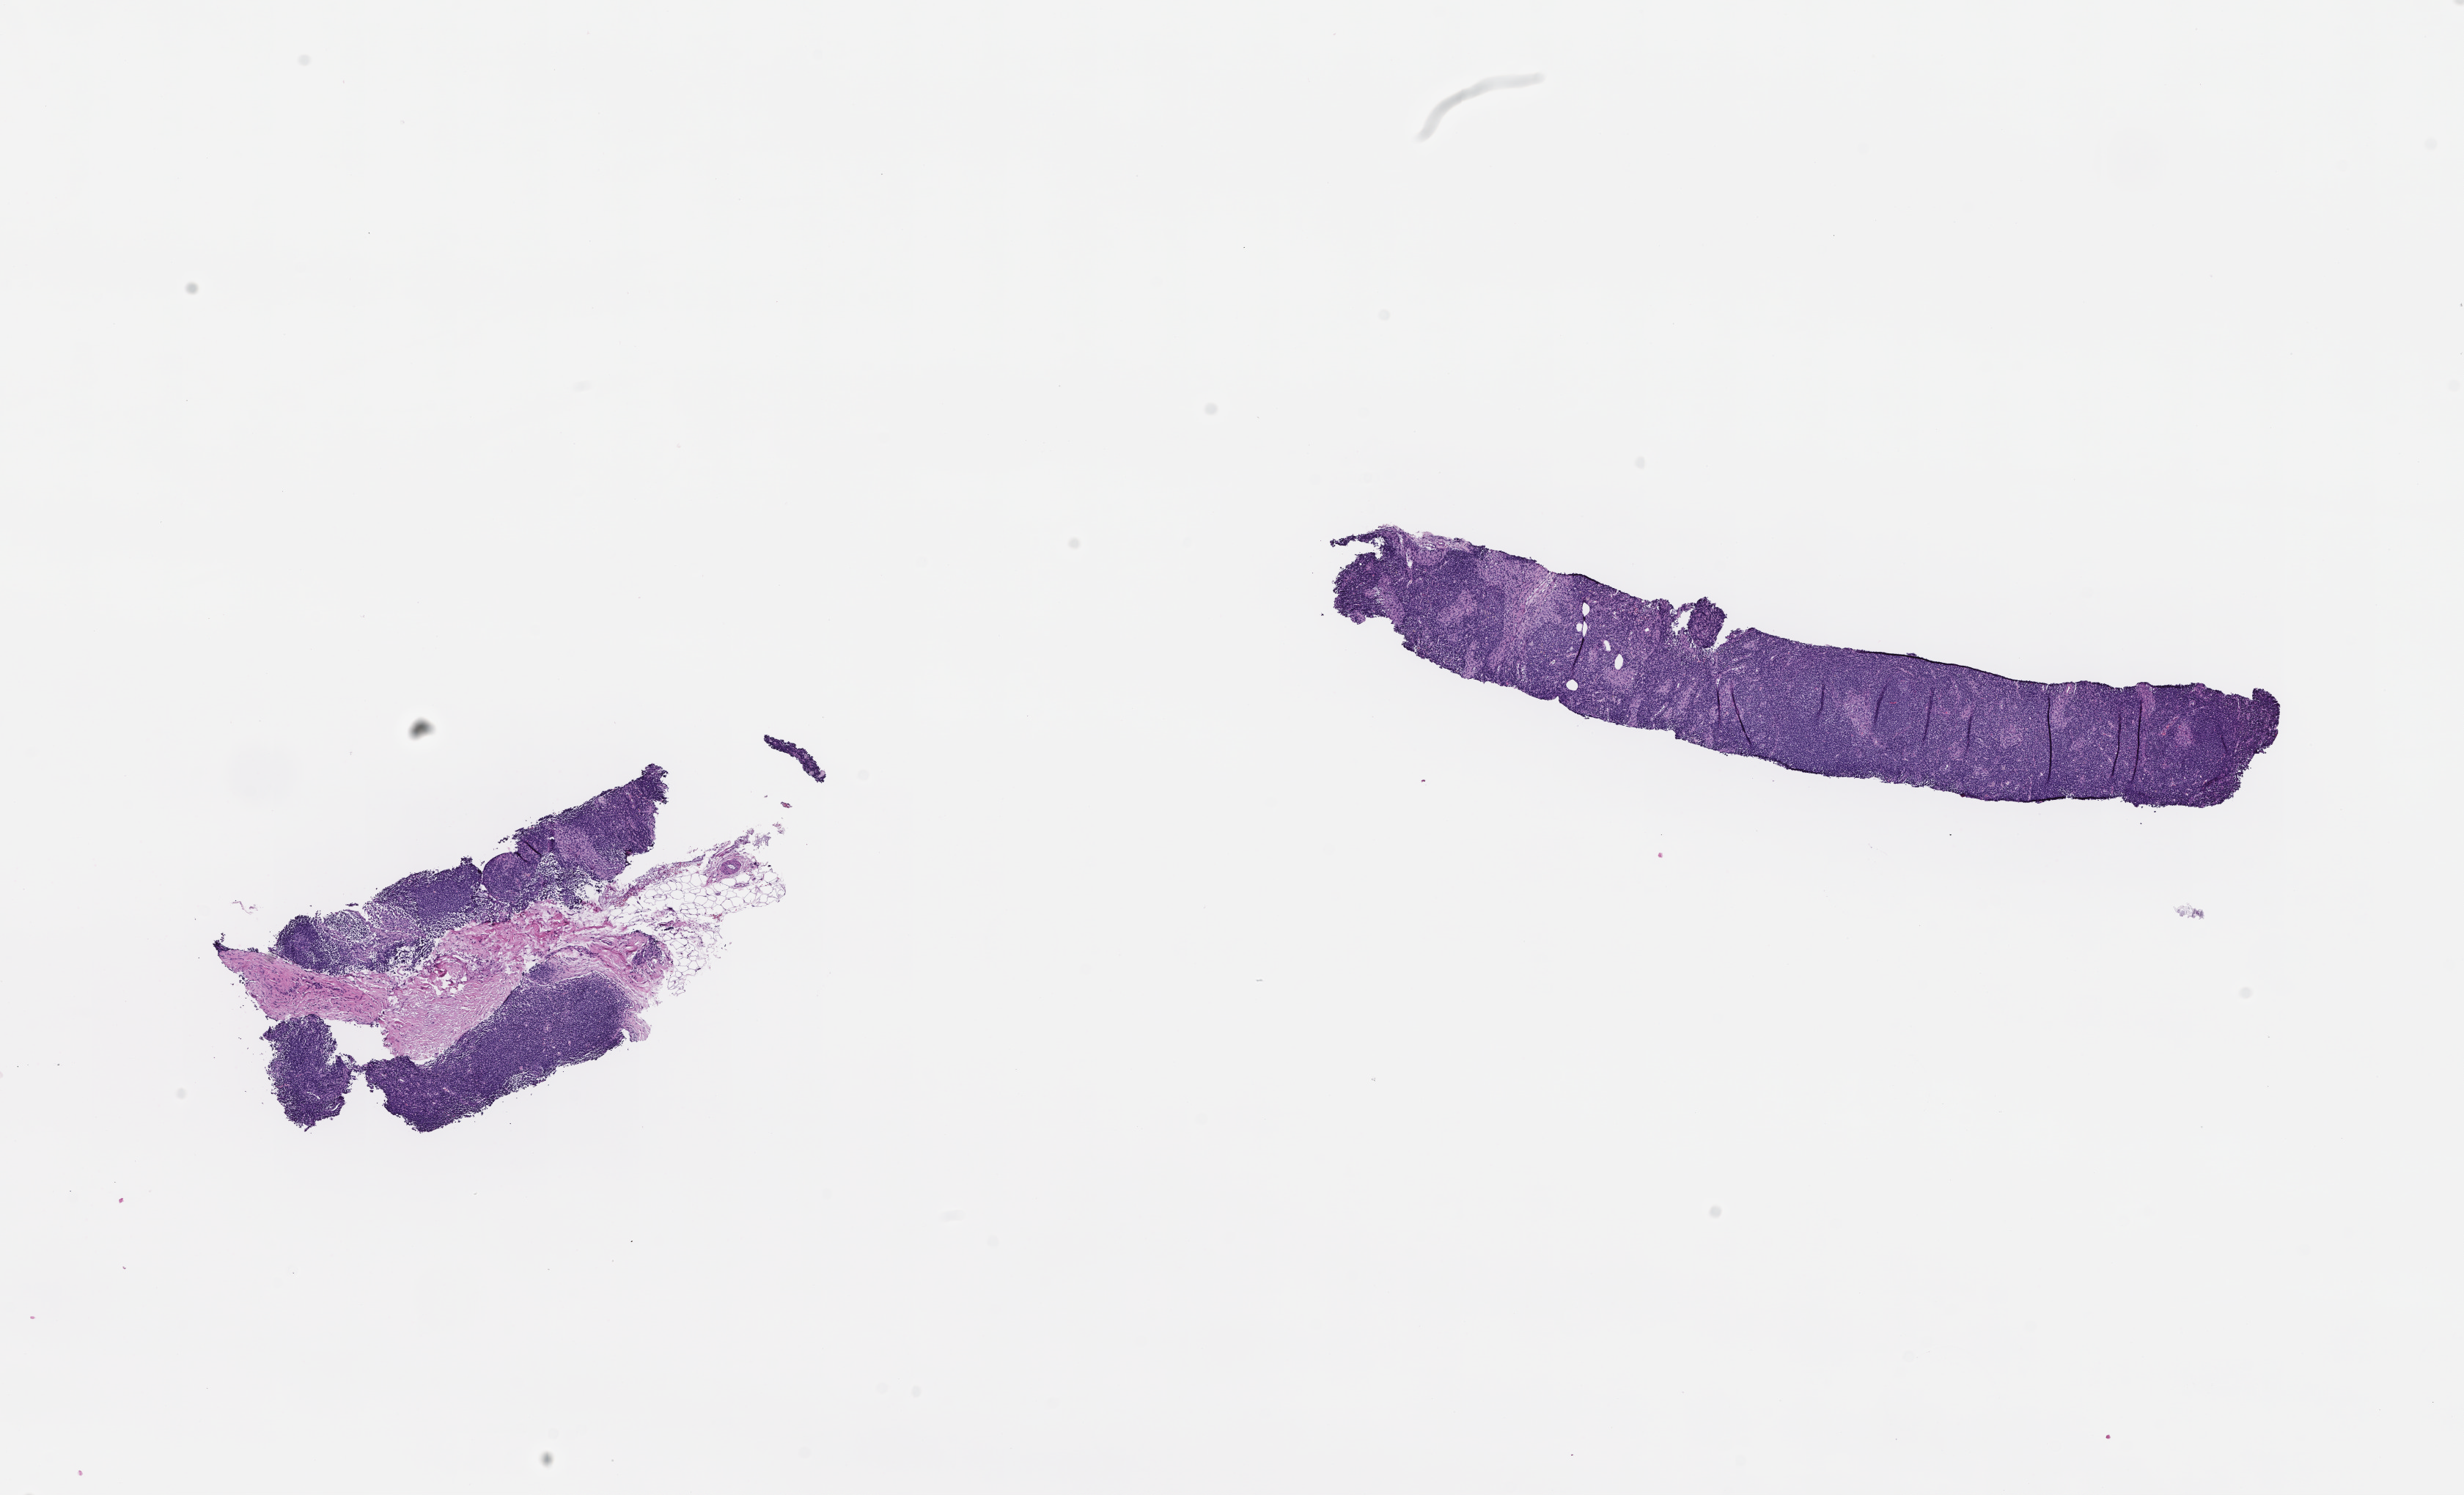
Whole-slide image, haematoxylin and eosin stain — shown as a low-resolution overview of the whole scanned area (about 13.6 x 8.2 mm). Formalin-fixed paraffin-embedded section. Patient: male.
This section: metastasis (sampled organ not recorded). Primary diagnosis of the patient: Melanoma.